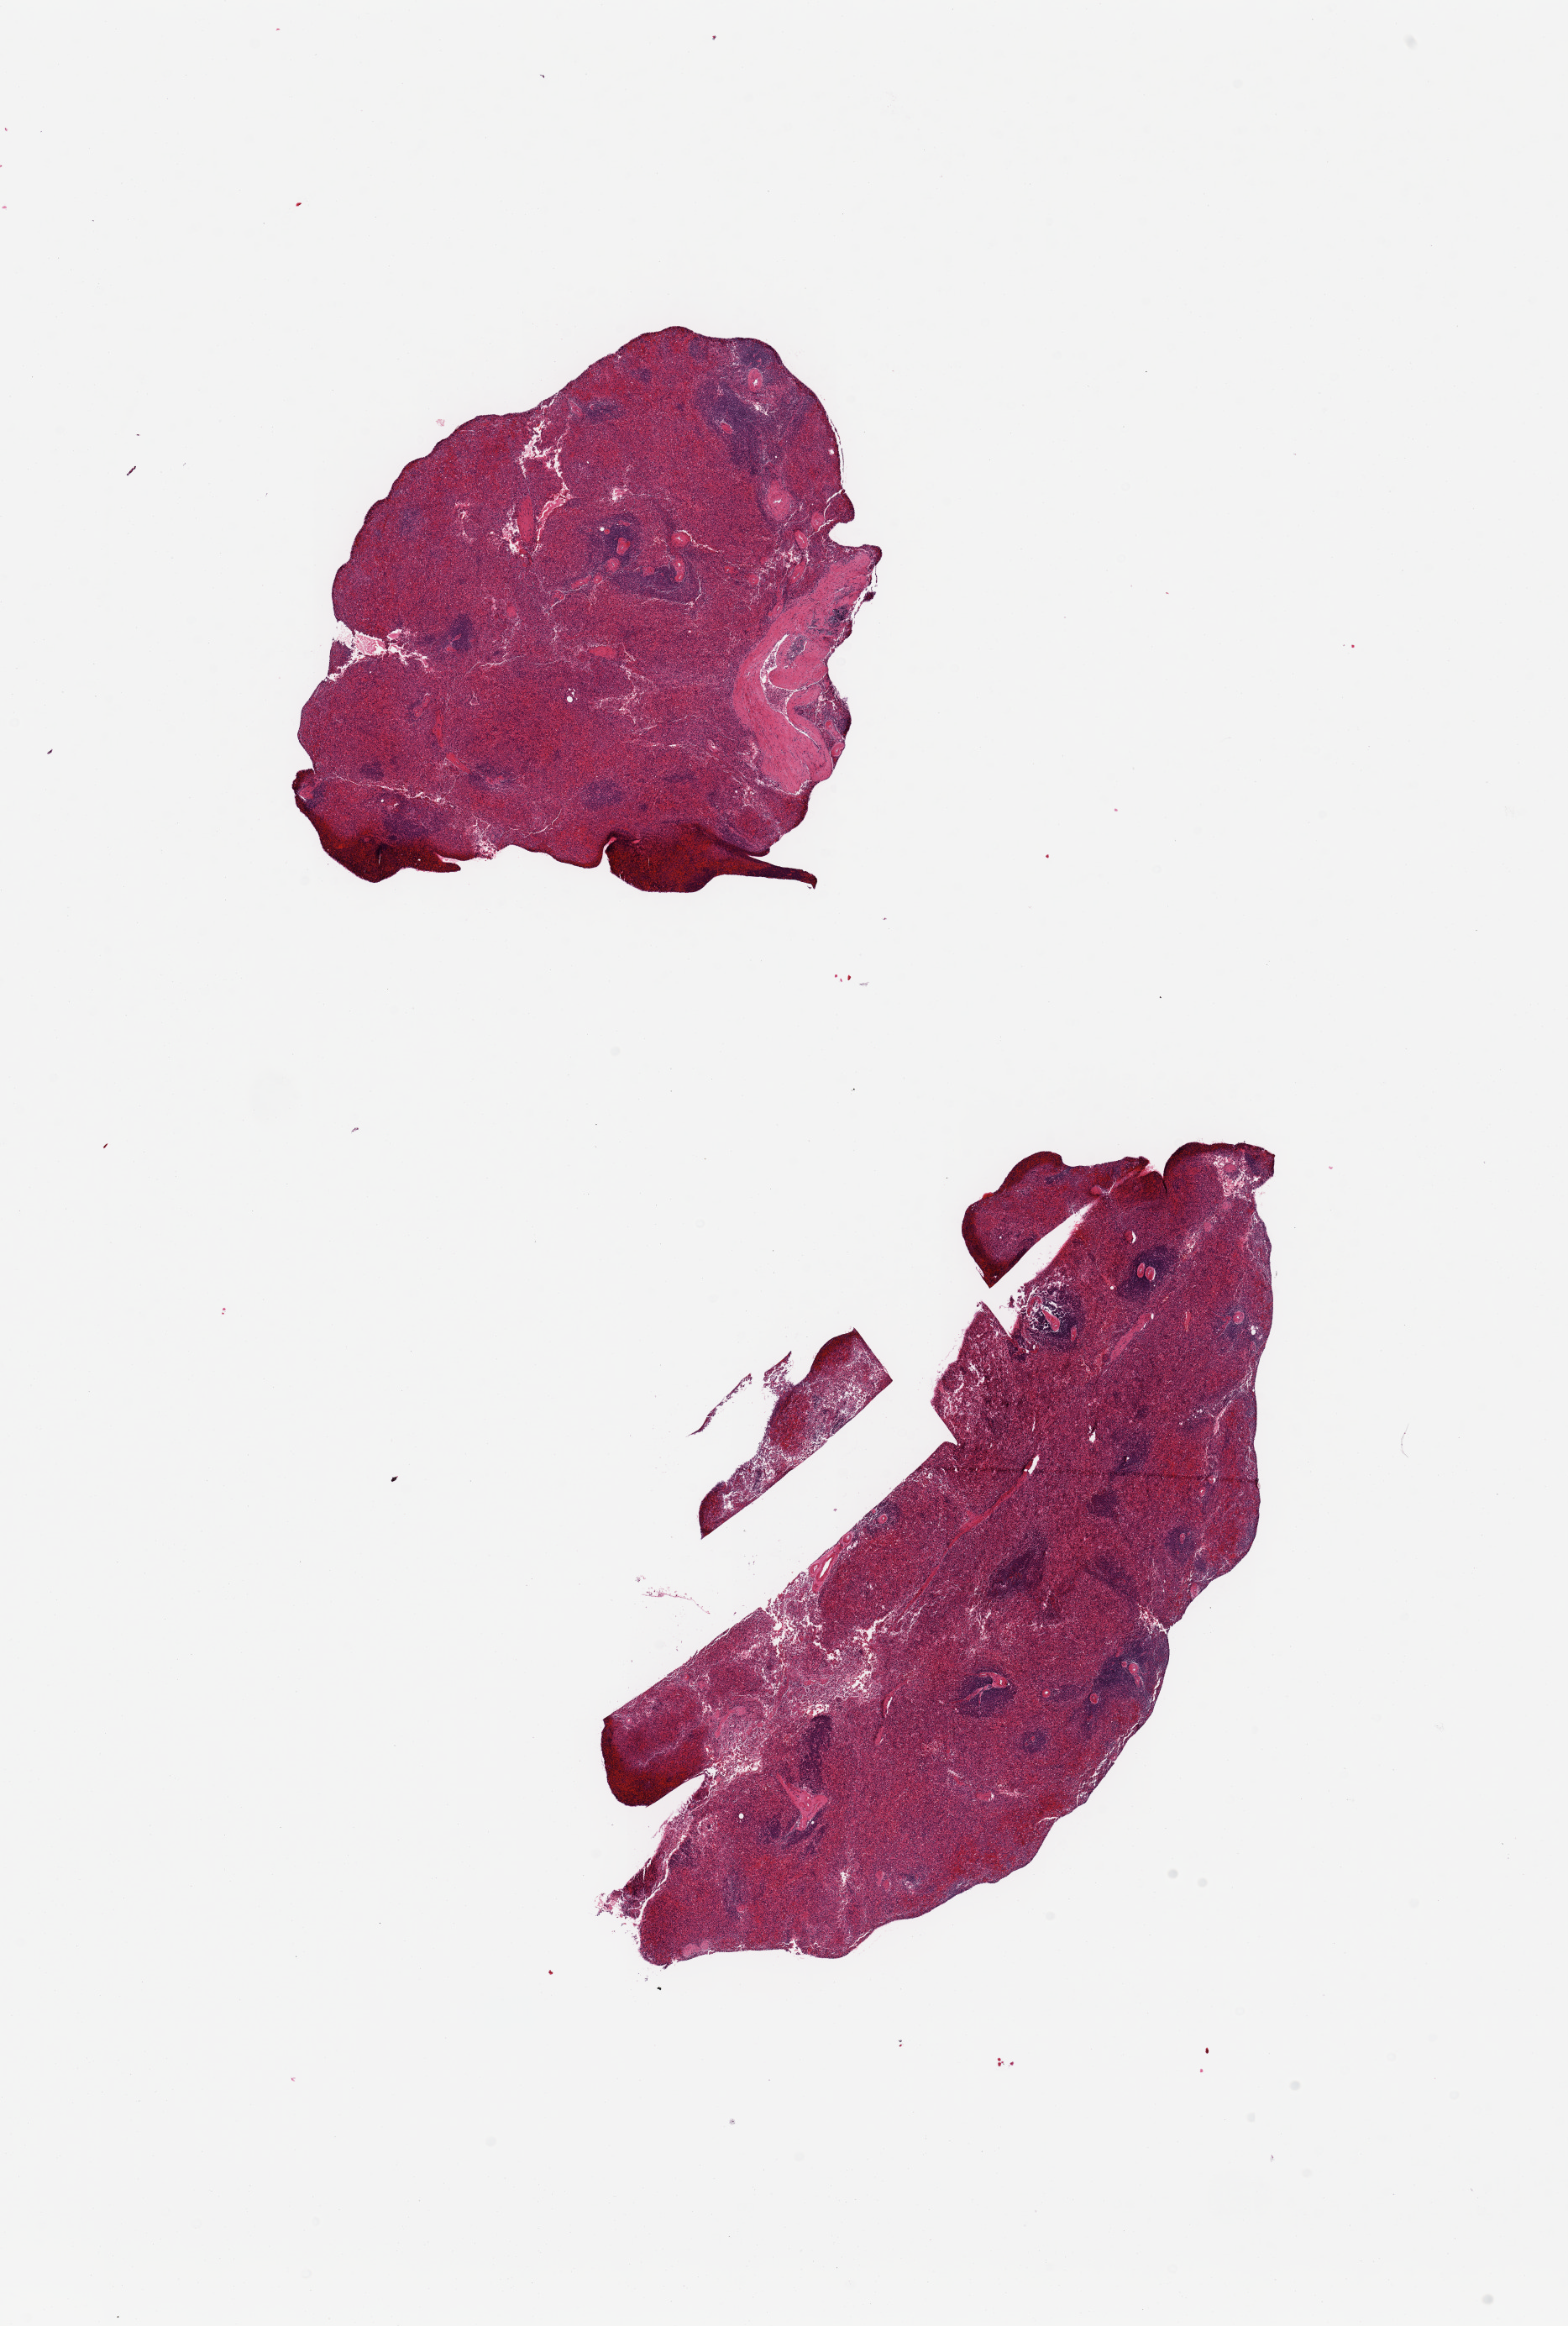
Hematoxylin and eosin (H&E) whole-slide image, low-resolution overview of the scanned area, about 14.8 x 21.9 mm; PAXgene-fixed, paraffin-embedded tissue; sampled site (target tissue): spleen; donor tissue sample. Donor: male.
Review note (as recorded): 2 pieces, no abnormalities.